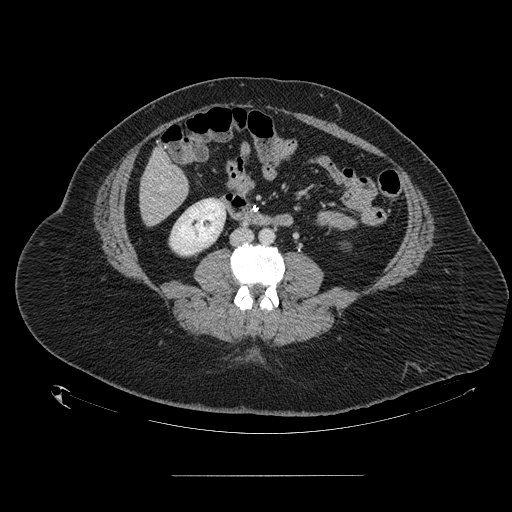
Contrast-enhanced abdominal CT, one axial slice. Position 28 of 164 along the scan axis. Intravenous contrast given. Soft-tissue window (W 400 / L 40 HU). 512 × 512 image matrix, field of view 495 × 495 mm. Female patient, age 52 years. Case-level facts recorded for this patient, not image findings: diagnosis: colorectal cancer liver metastases, imaged before liver resection; multiple liver metastases: yes; largest metastasis: 3.5 cm.
Outlined on this slice (outlined manually by an expert reader):
- hepatic veins: box from (x=160, y=187) to (x=162, y=189) px
- liver: (x=141, y=151)–(x=188, y=225)